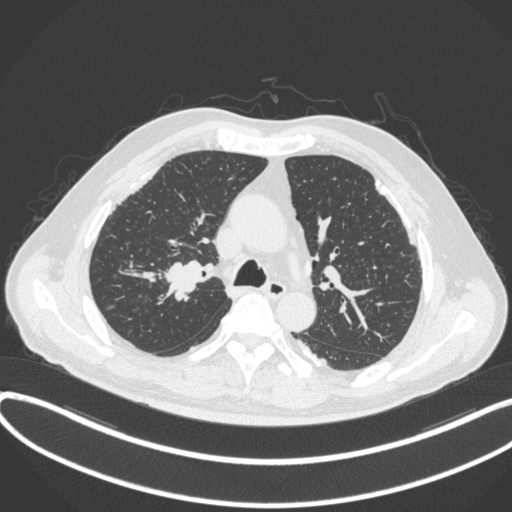
Chest CT, one axial slice; slice 287 of 455 in the series (ordered by position); reconstruction kernel B31f; lung window (W 1500 / L -600 HU); 1 mm slice thickness; 512 × 512 image matrix, field of view 400 × 400 mm. Patient: male, 58 years. From the clinical record (not read from this slice): clinical TNM (as recorded): T1c N0 M0.
Outlined on this slice (rectangle marked by the reading radiologist):
- lung tumour (recorded histology: squamous cell carcinoma): bounding box (x1, y1, x2, y2) in pixels: (162, 255, 205, 303)